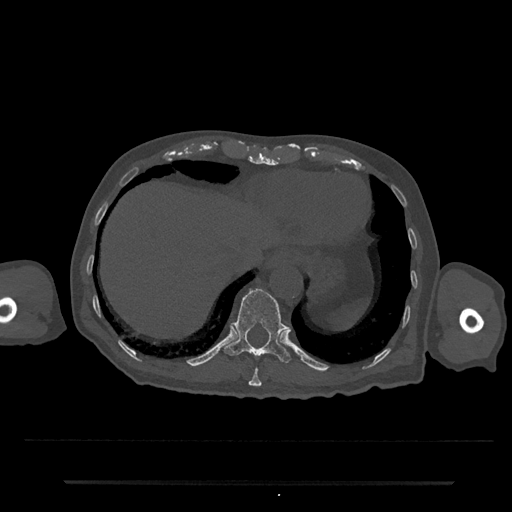
CT including the spine, one axial slice. Position 264 of 797 along the scan axis. Reconstruction kernel Br40s/3. 120 kVp. Bone window (W 1800 / L 400 HU). 0.5 mm slice thickness. 512 × 512 image matrix. Male patient, age 74 years. Case-level facts recorded for this patient, not image findings: primary cancer: prostate.
Structures marked on this image (semi-automatically segmented with operator editing):
- T10 vertebra: bounding box <248,367,262,387> (left, top, right, bottom; pixels)
- T11 vertebra: <224,289,291,363>